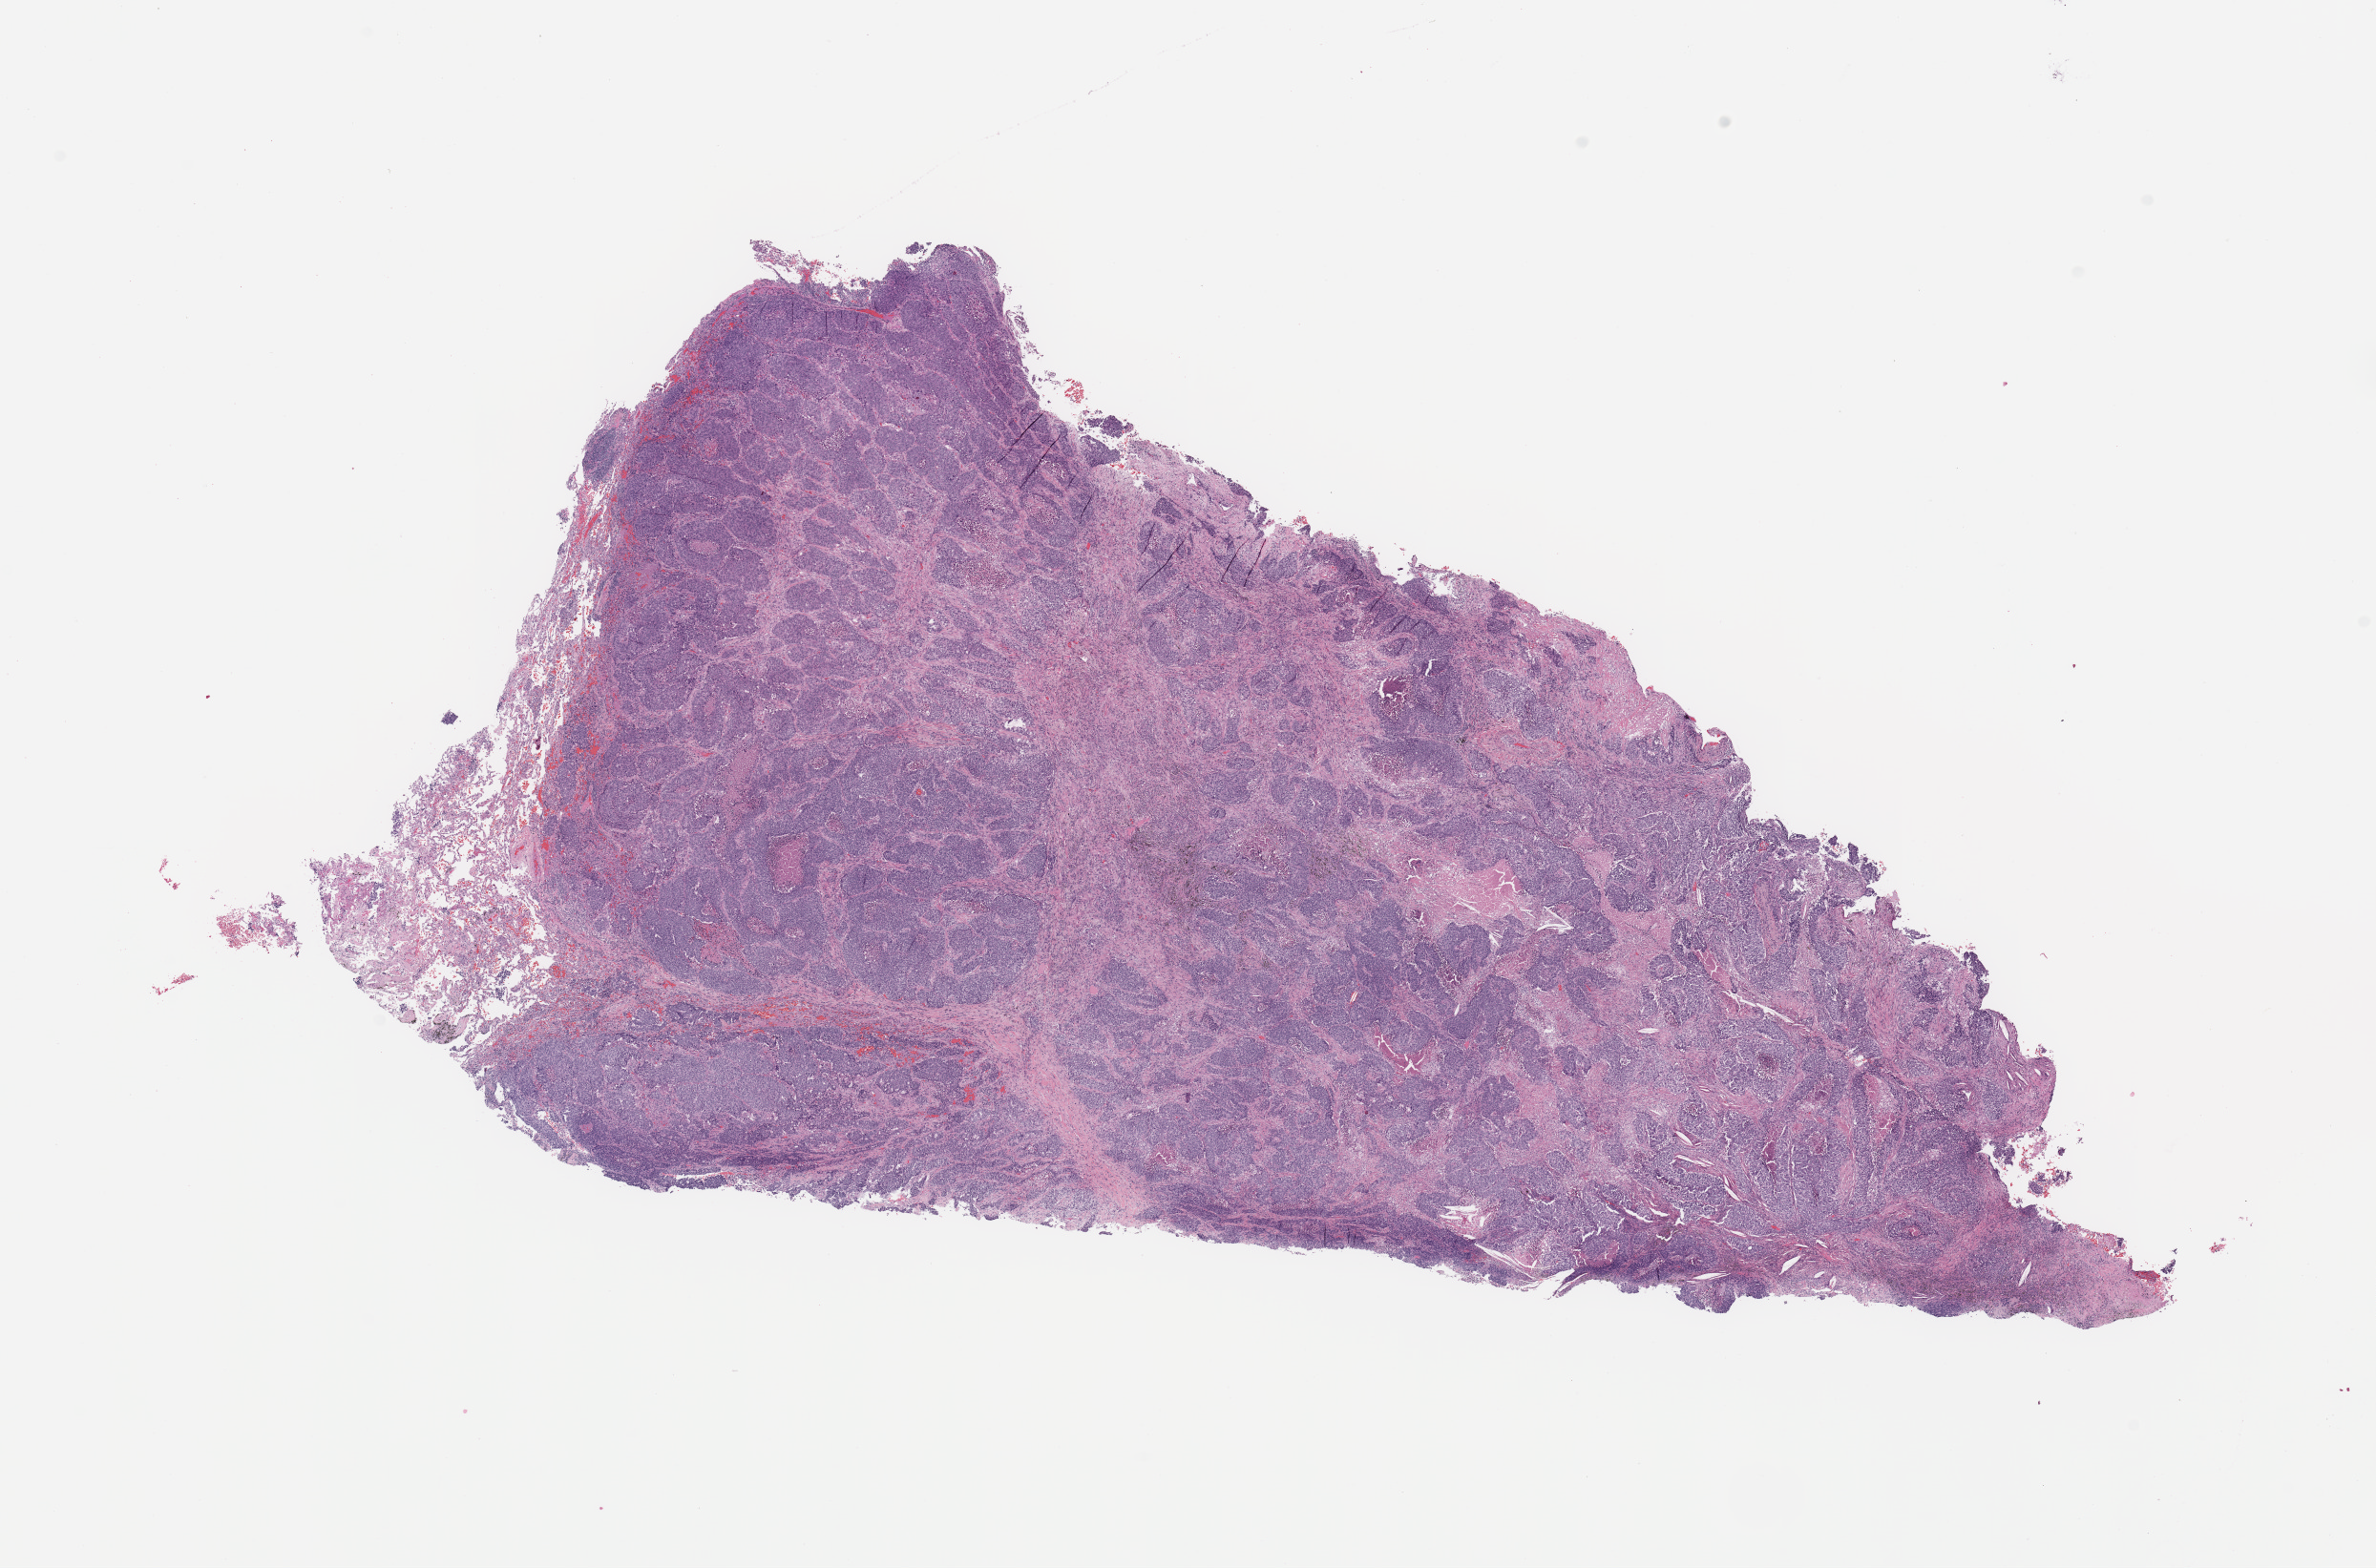
Hematoxylin and eosin (H&E) stained whole-slide image — shown as a low-resolution overview of the whole scanned area (about 19.7 x 13.0 mm); lung, tumour tissue. 59-year-old male patient.
Histologic diagnosis: Squamous cell carcinoma, NOS.